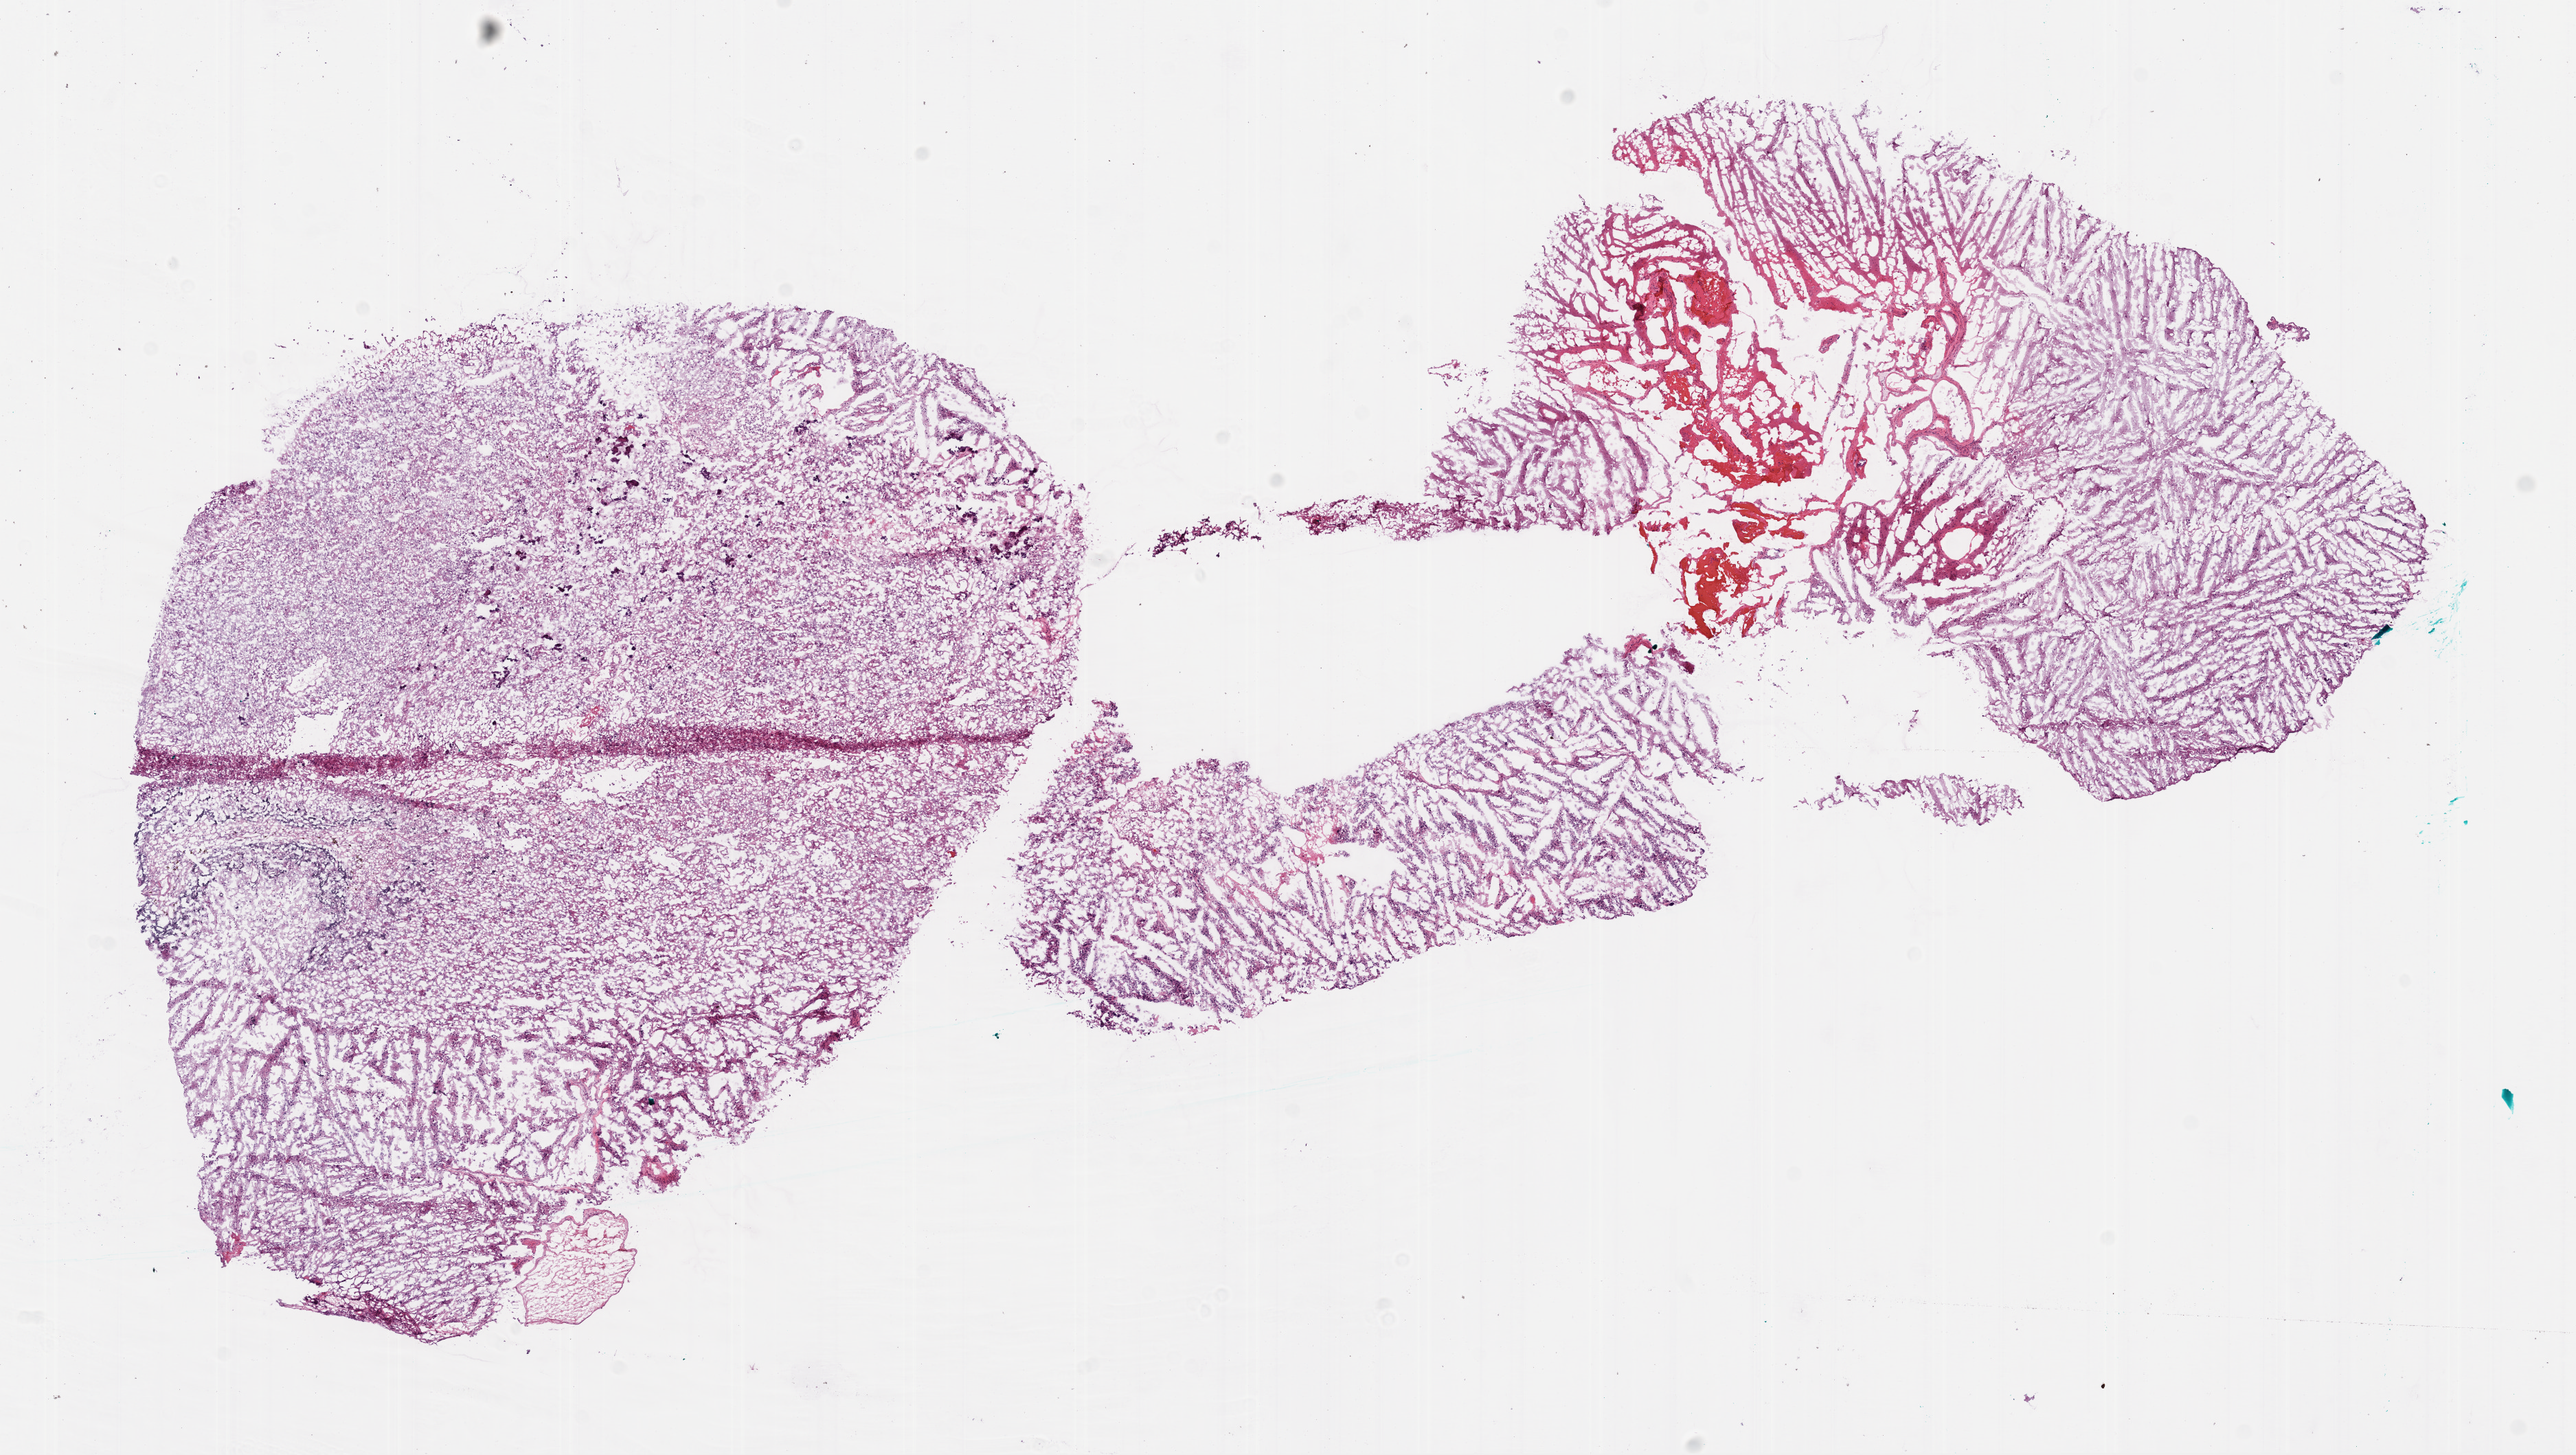
H&E-stained whole-slide image — low-resolution overview of the scanned area, about 15.0 x 8.5 mm (slide scanned at 20x); frozen section from the bottom of the tissue portion; sample: primary tumour, brain. Female patient; age at initial diagnosis 38 years. Pathologist review of this section (percent, as recorded): tumour cells 90%, tumour nuclei 100%, normal cells 0%, stromal cells 0%, necrosis 10%. Inflammatory infiltration, as recorded: lymphocyte infiltration 0%.
Diagnosis: Glioblastoma.